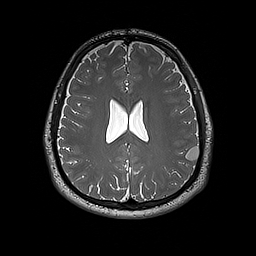
Brain MRI from a brain-tumour surgery series, one axial slice; slice 77 of 192 in the series (ordered by position); 256 × 256 image matrix, field of view 250 × 250 mm. Case-level facts recorded for this patient, not image findings: histopathology: Dysembryoplastic neuroepithelial tumor; WHO grade: 1; IDH mutation: no.
Annotated regions visible in this slice (expert manual segmentation):
- tumour: box from (x=186, y=146) to (x=200, y=161) px